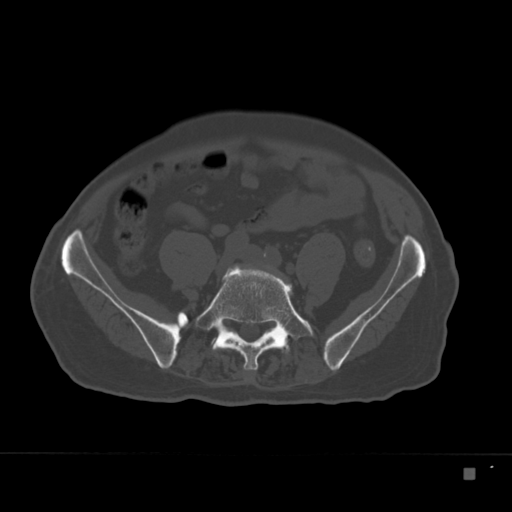
CT including the spine, one axial slice; slice 23 of 332 in the series (ordered by position); 120 kVp; bone window (W 1800 / L 400 HU); 1.5 mm slice thickness; 512 × 512 image matrix, field of view 389 × 389 mm. Patient: male, 72 years. Case-level facts recorded for this patient, not image findings: primary cancer: skeletal.
Outlined on this slice (semi-automatically segmented with operator editing):
- L5 vertebra: bounding box <194,265,314,370> (left, top, right, bottom; pixels)